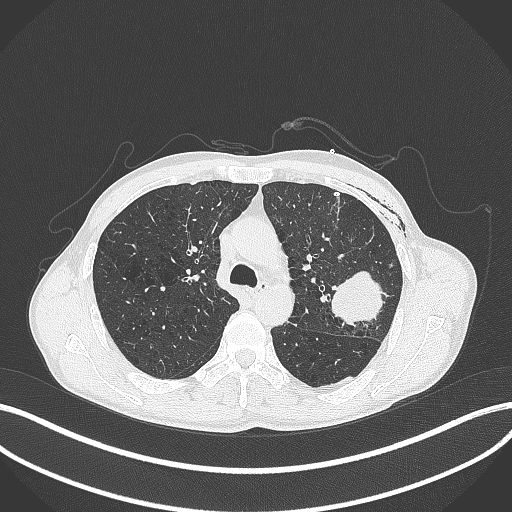
Chest CT, one axial slice; position 277 of 457 along the scan axis; reconstruction kernel B70f; 120 kVp; lung window (W 1500 / L -600 HU); 1 mm slice thickness; 512 × 512 image matrix, field of view 400 × 400 mm. Male patient, age 58 years. From the clinical record (not read from this slice): clinical TNM (as recorded): T3 N0 M0.
Outlined on this slice (bounding box drawn by a radiologist):
- lung tumour (recorded histology: adenocarcinoma): bounding box (x1, y1, x2, y2) in pixels: (329, 269, 390, 330)